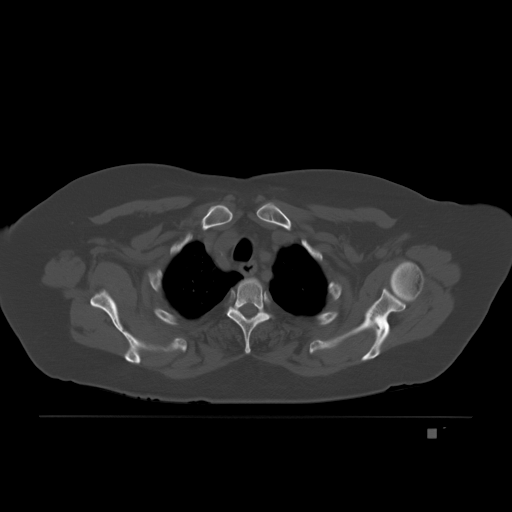
CT including the spine, one axial slice; position 166 of 221 along the scan axis; bone window (W 1800 / L 400 HU); 3 mm slice thickness; 512 × 512 image matrix. Patient: female, 63 years. Case-level facts recorded for this patient, not image findings: primary cancer: breast.
Outlined on this slice (semi-automatically segmented with operator editing):
- T3 vertebra: bounding box <230,311,270,325> (left, top, right, bottom; pixels)